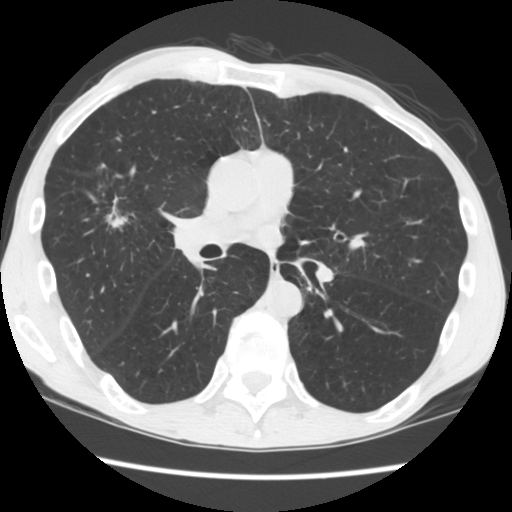
Low-dose screening chest CT, axial slice; second annual screen; lung window (W 1500 / L -600 HU); 2.5 mm slice thickness; standard (soft-tissue) reconstruction kernel (STANDARD); 512 × 512 image matrix. Male participant, aged 56 years at enrolment.
Expert-annotated lung lesion, box from (x=80, y=154) to (x=147, y=232) px. The screening reader recorded 2 non-calcified nodules or masses ≥4 mm on this exam; which of them this box marks is not recorded. Official screen result: positive, change unspecified: nodule(s) >= 4 mm or enlarging nodule(s), mass(es), or other non-specific abnormalities suspicious for lung cancer. Later outcome: lung cancer diagnosed 101 days after this screen — squamous cell carcinoma, NOS, right upper lobe, right middle lobe, well differentiated (G1), stage IA (AJCC 6th edition), 27 mm at pathology.